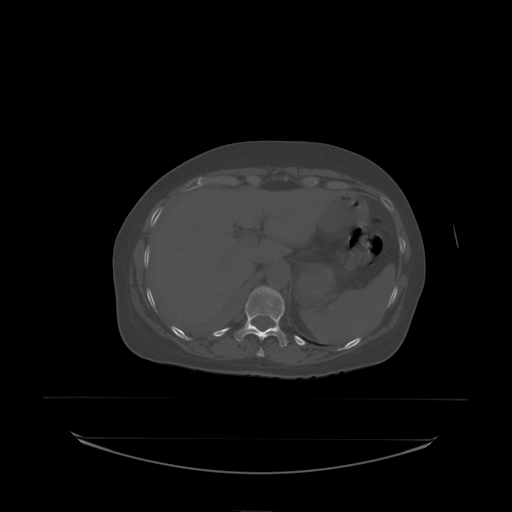
CT including the spine, one axial slice; position 104 of 242 along the scan axis; bone window (W 1800 / L 400 HU); 2.5 mm slice thickness; 512 × 512 image matrix. Patient: female, 53 years. From the clinical record (not read from this slice): primary cancer: lung; vertebrae with lytic lesions (as recorded): T7, L1.
Structures marked on this image (semi-automatically segmented with operator editing):
- T11 vertebra: box from (x=235, y=287) to (x=285, y=338) px